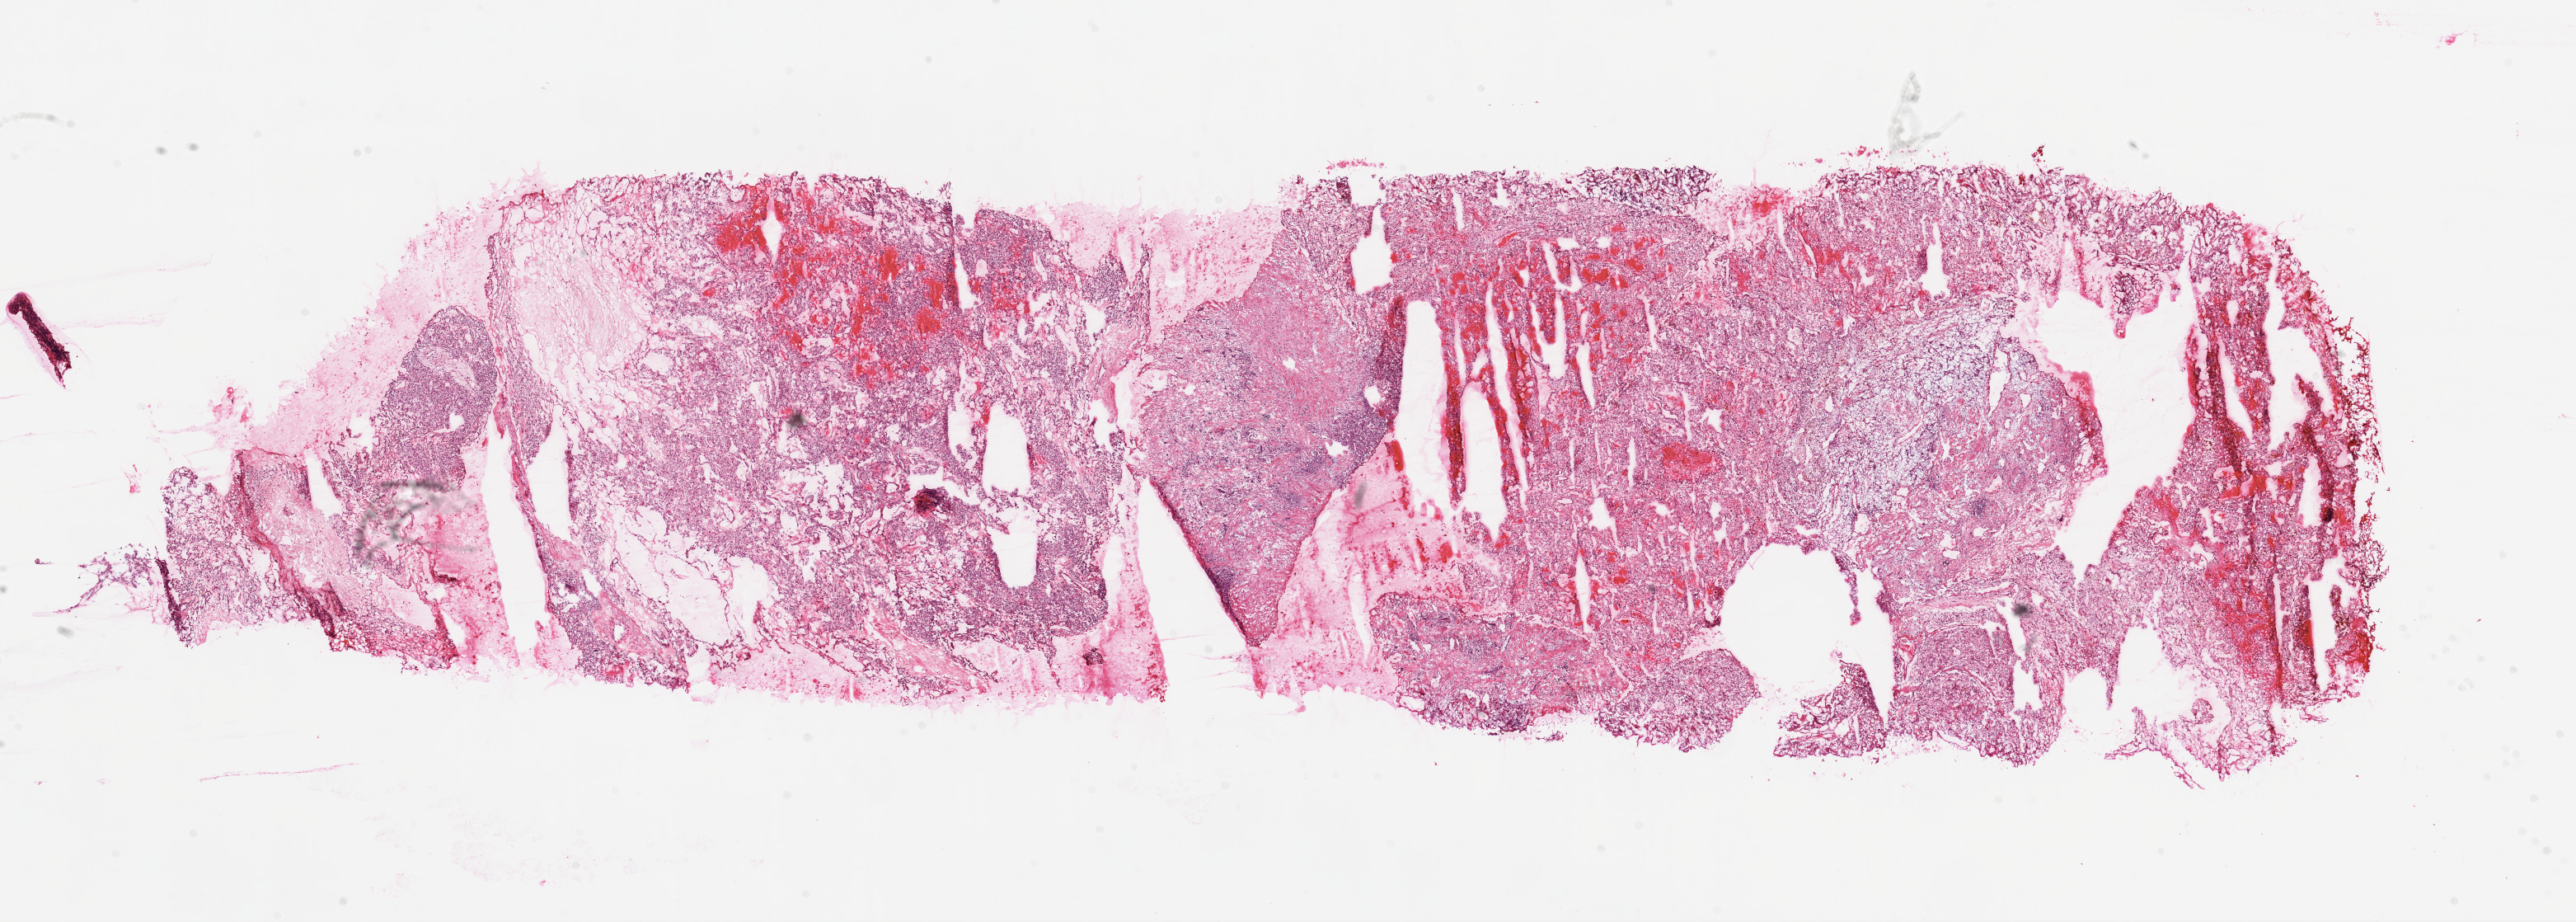
Digitized Hematoxylin and eosin (H&E) stained tissue section (whole slide) — whole scanned area (about 25.1 x 9.0 mm, slide scanned at 20x) shown as a low-resolution overview, frozen section from the top of the tissue portion, kidney, primary tumour sample. Patient: male, age at initial diagnosis 38 years. Histologic grade: G2 (moderately differentiated). Pathologist review of this section (percent, as recorded): tumour cells 70%, tumour nuclei 80%, normal cells 0%, stromal cells 30%, necrosis 0%.
AJCC pathologic stage: I. Histologic diagnosis: Clear cell adenocarcinoma, NOS. TNM: T1a NX M0. Laterality: right.